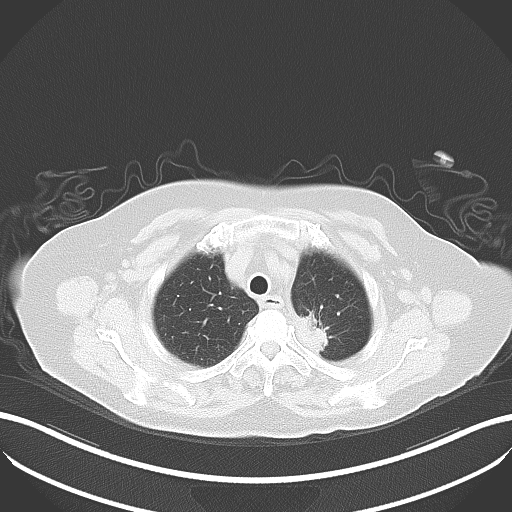
Chest CT, one axial slice. Position 34 of 42 along the scan axis. Lung window (W 1500 / L -600 HU). 512 × 512 image matrix. Patient: female, 81 years. From the clinical record (not read from this slice): clinical TNM (as recorded): T2a N0 M0.
Annotated regions visible in this slice (rectangle marked by the reading radiologist):
- lung tumour (recorded histology: adenocarcinoma): bounding box (x1, y1, x2, y2) in pixels: (292, 301, 331, 355)